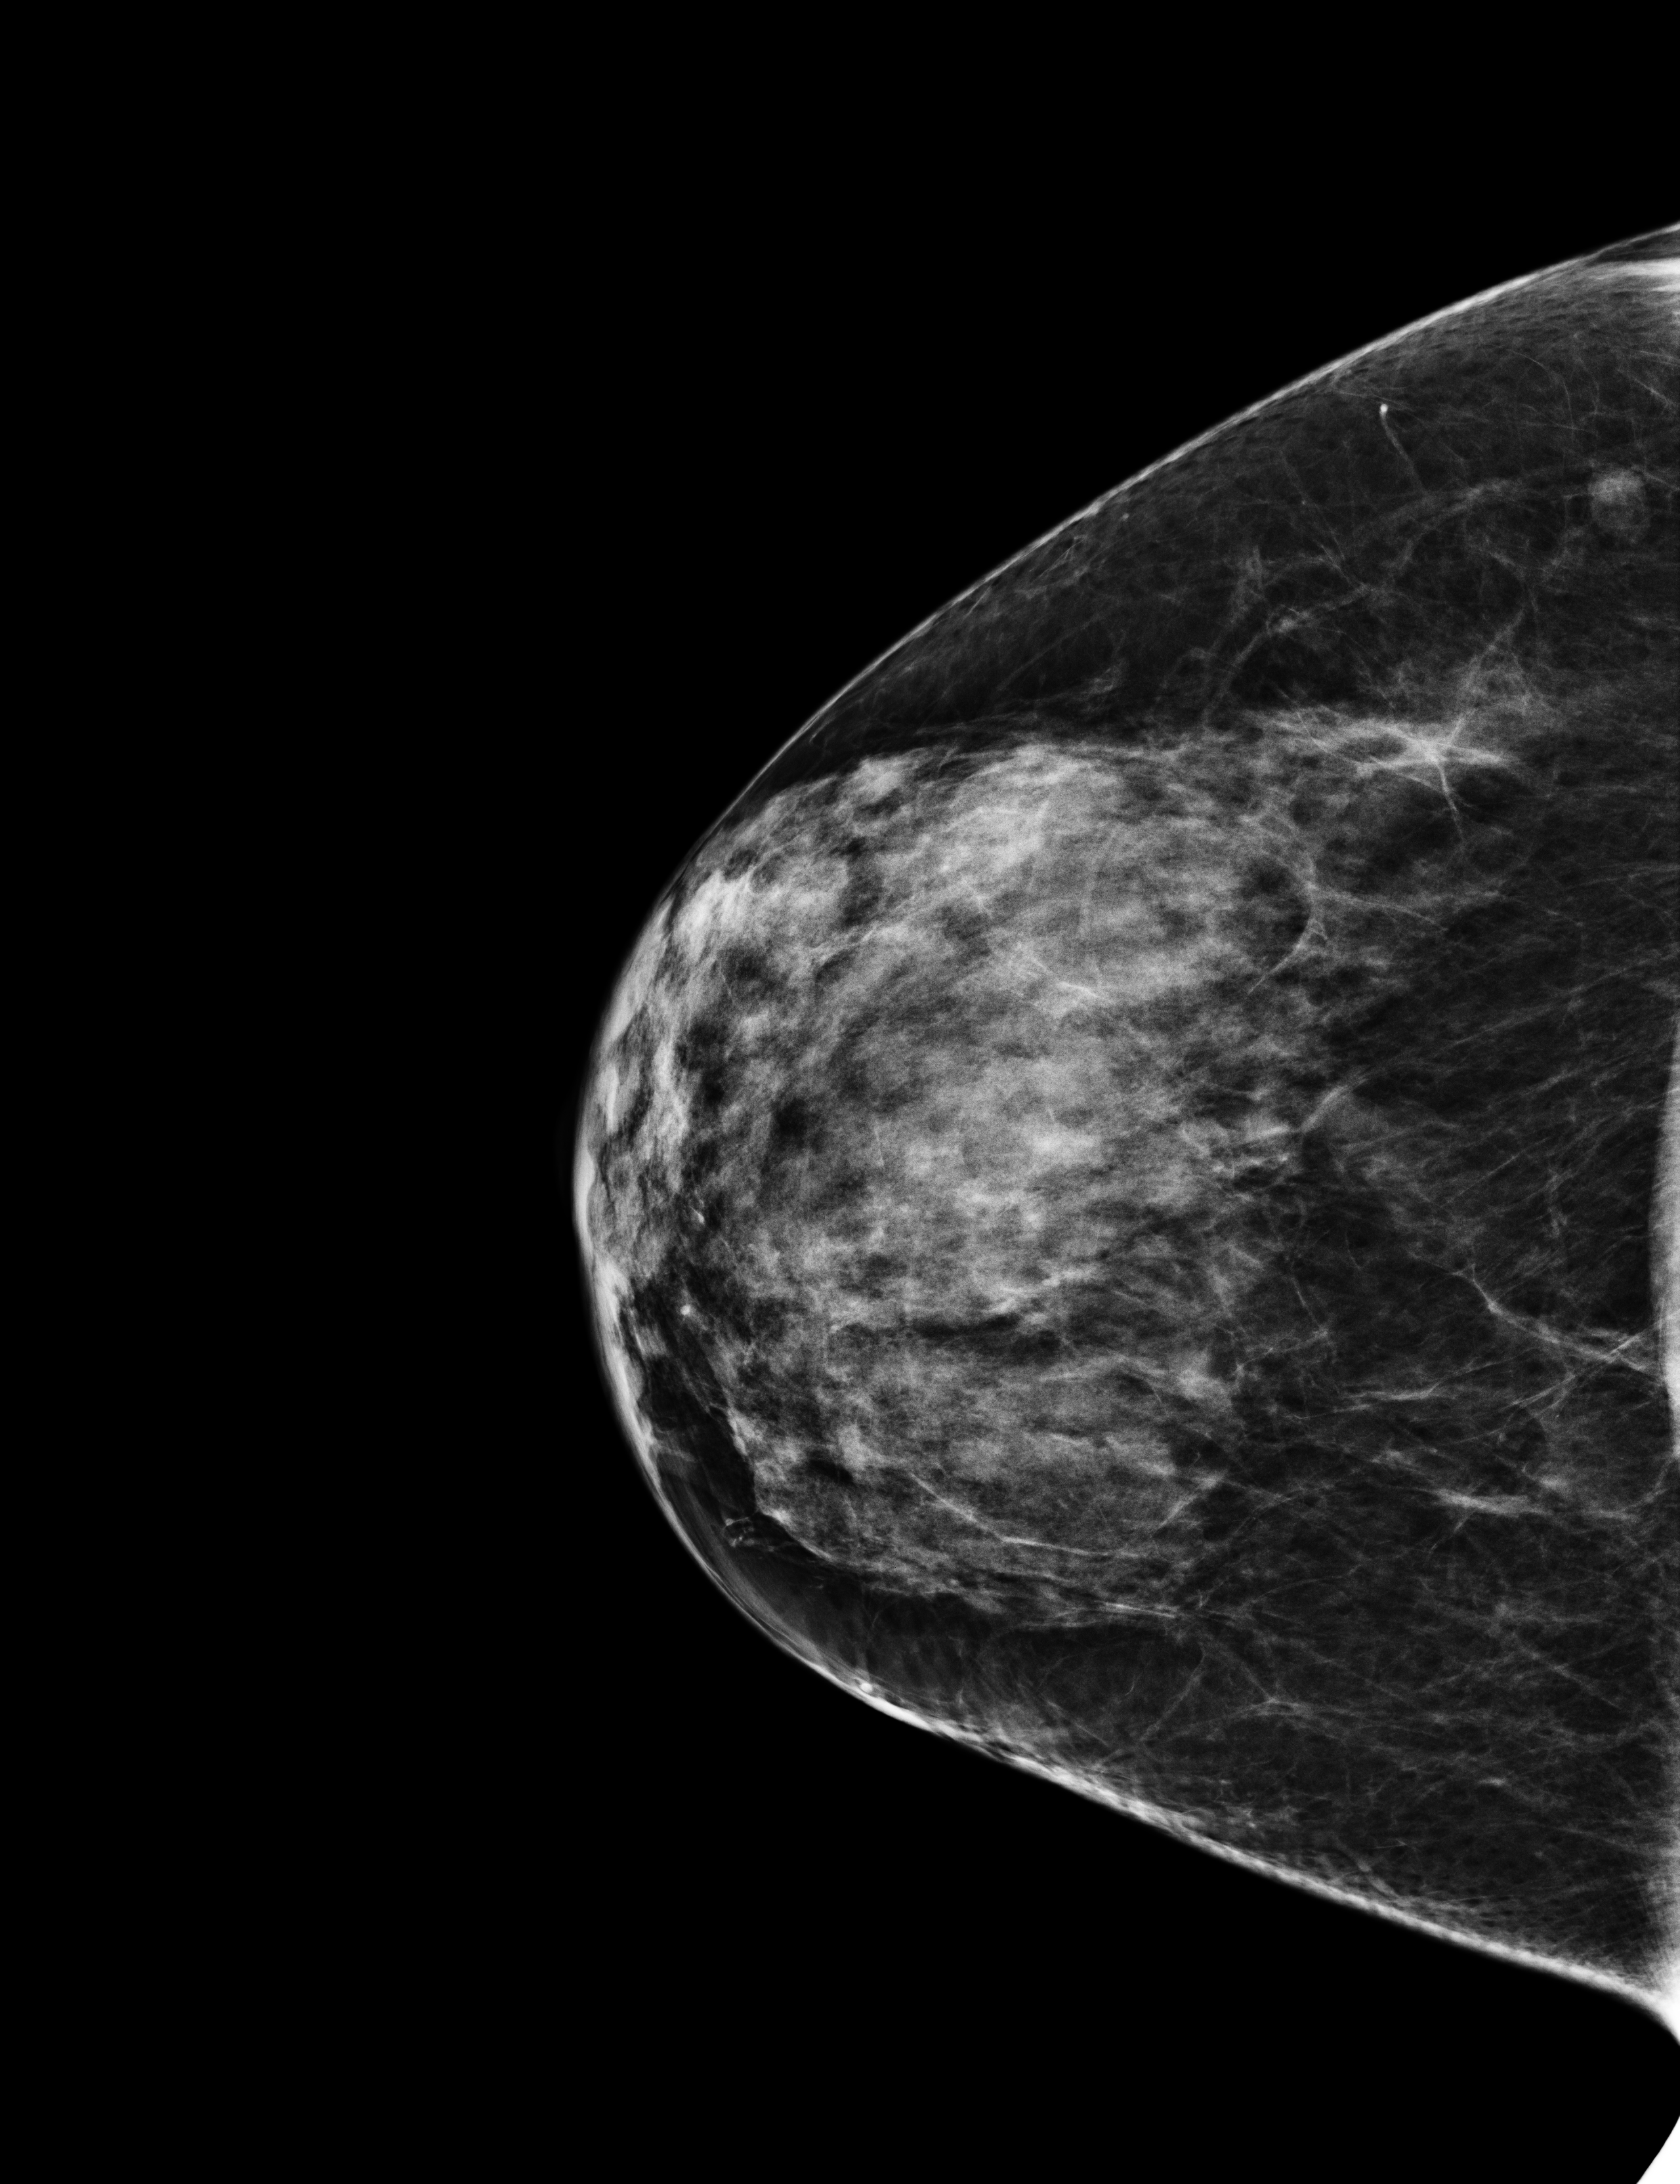
Screening examination, compressed breast thickness 58 mm. Patient aged 54 years (female).
Image type: full-field digital mammogram. Breast: right. Projection: craniocaudal (CC) view. BI-RADS breast density category at the screening exam (both breasts, scale 1–4): 3. Final BI-RADS assessment for this screening round (tomosynthesis exam, both breasts): category 1. Recall: no recall after this screen.